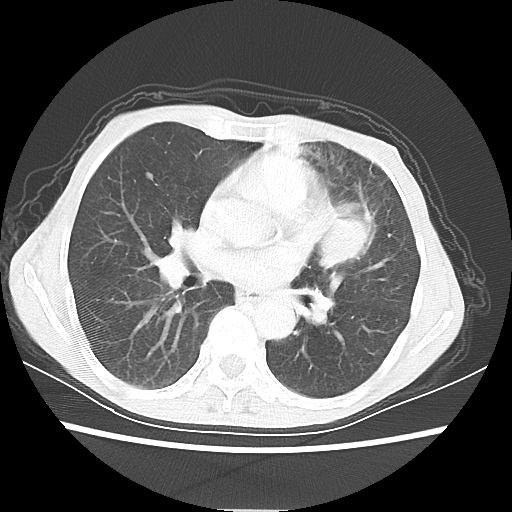
Chest CT, one axial slice; slice 31 of 56 in the series (ordered by position); 80 kVp; lung window (W 1500 / L -600 HU); 5 mm slice thickness; 512 × 512 image matrix. Female patient, age 60 years. From the clinical record (not read from this slice): clinical TNM (as recorded): T4 N1 M0.
Outlined on this slice (bounding box drawn by a radiologist):
- lung tumour (recorded histology: adenocarcinoma): bounding box (x1, y1, x2, y2) in pixels: (322, 200, 375, 275)